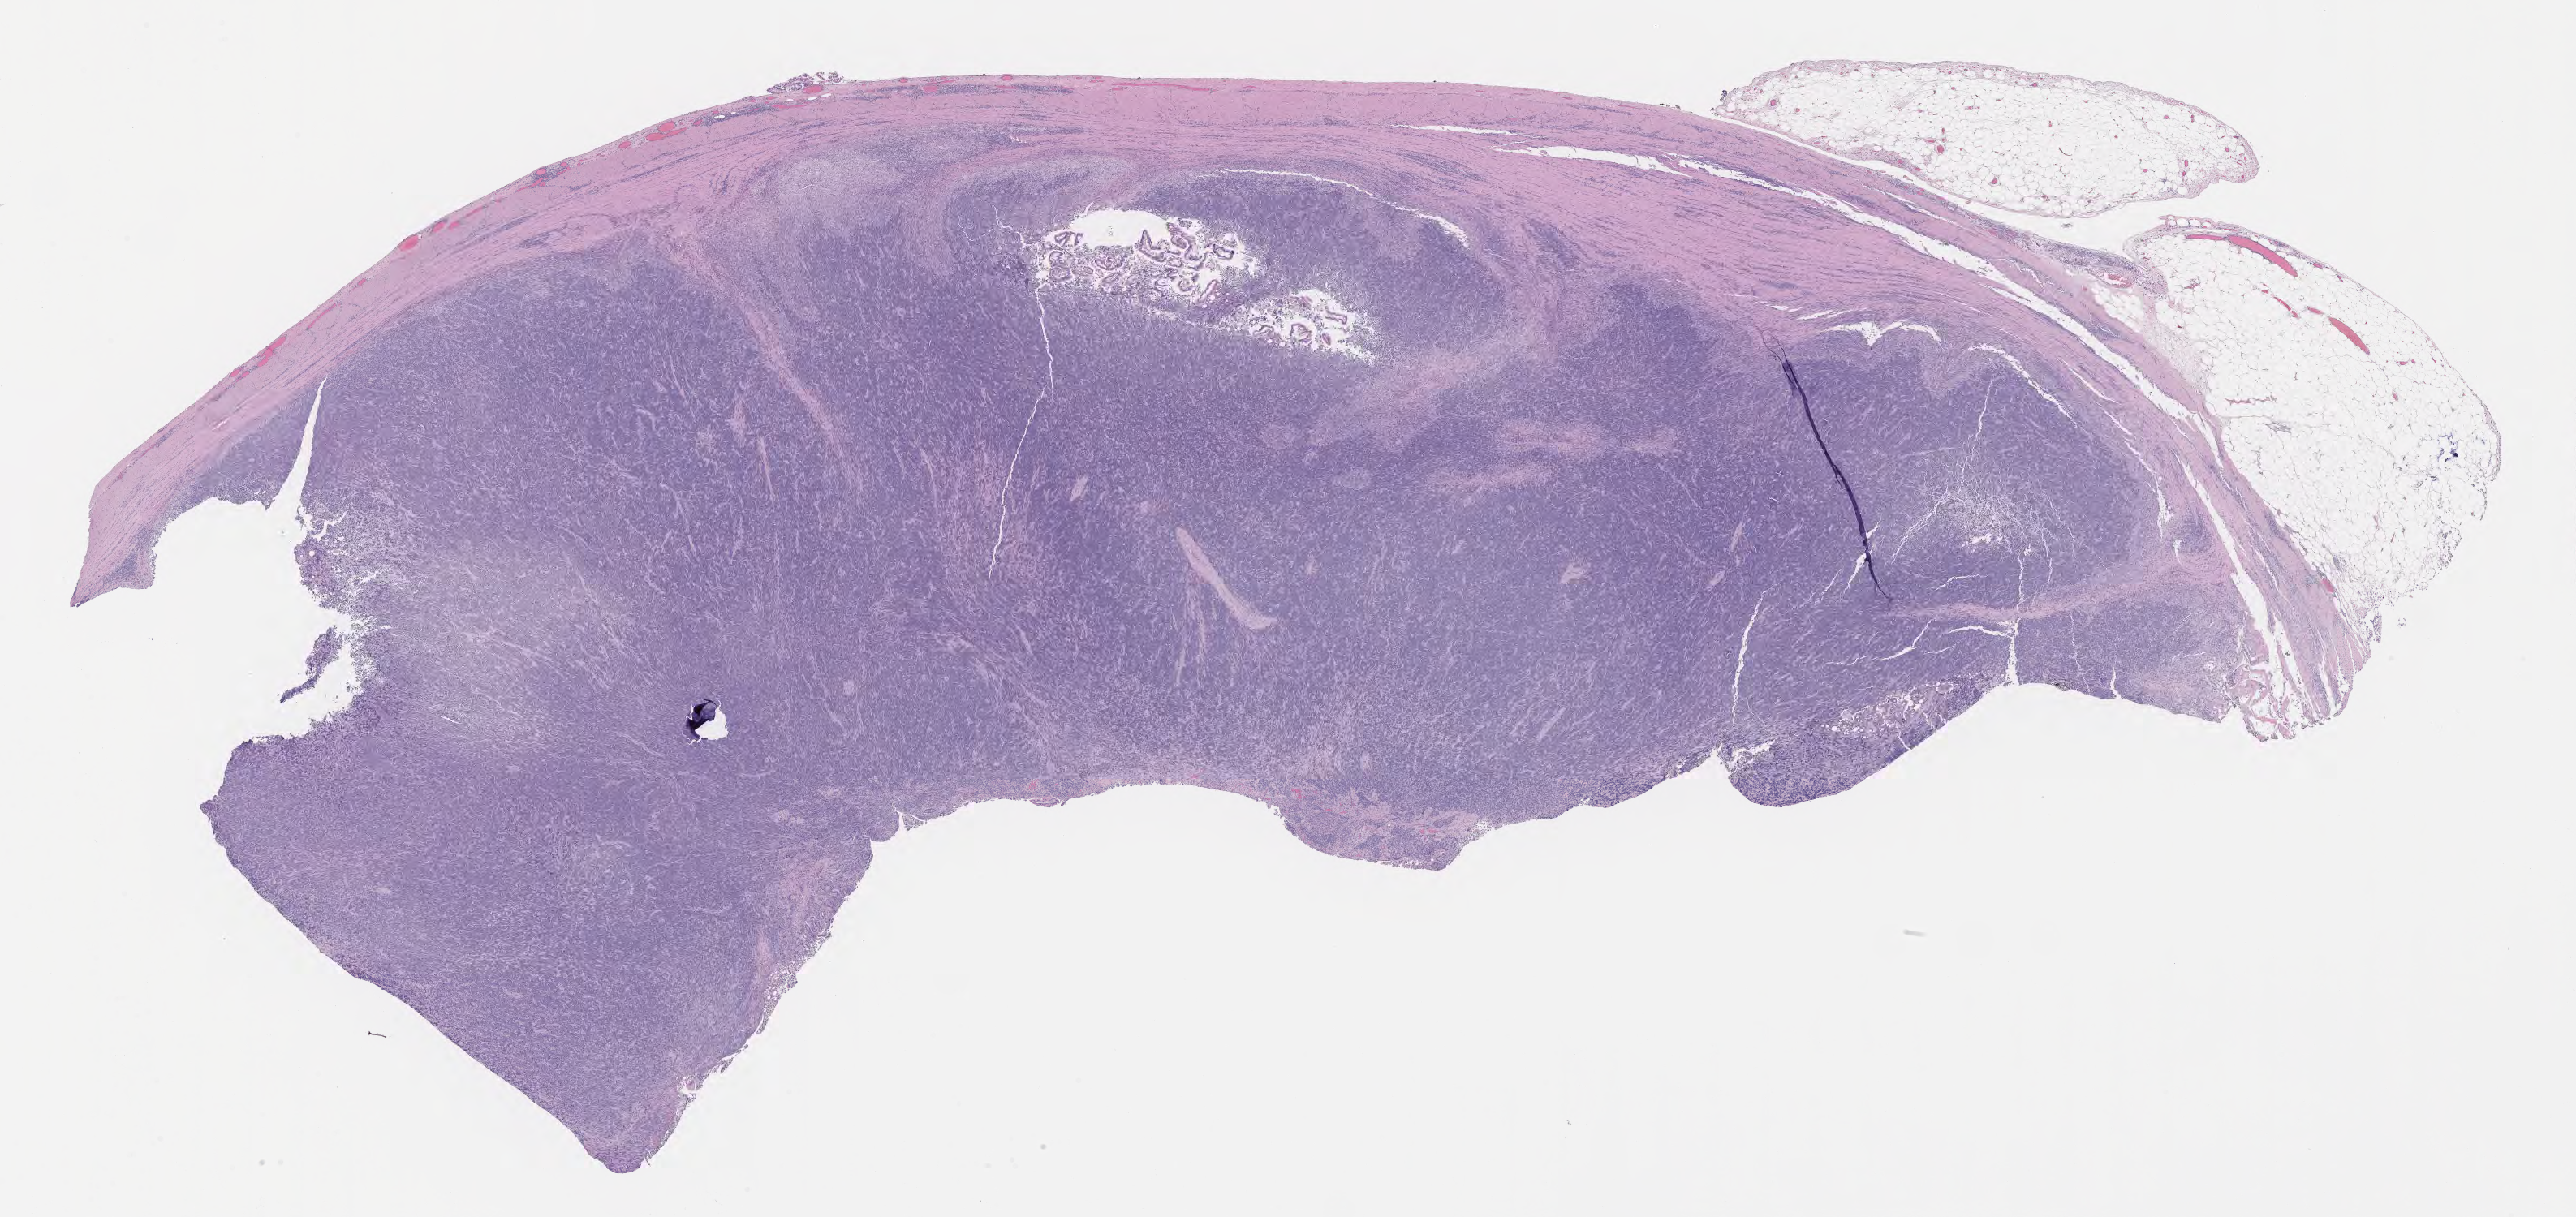
Whole-slide image, haematoxylin and eosin stain, a low-resolution overview of the entire scanned area, about 25.7 x 12.1 mm. Tumor tissue. Patient male; aged 70.
Histologic diagnosis: Neoplasm, uncertain whether benign or malignant.